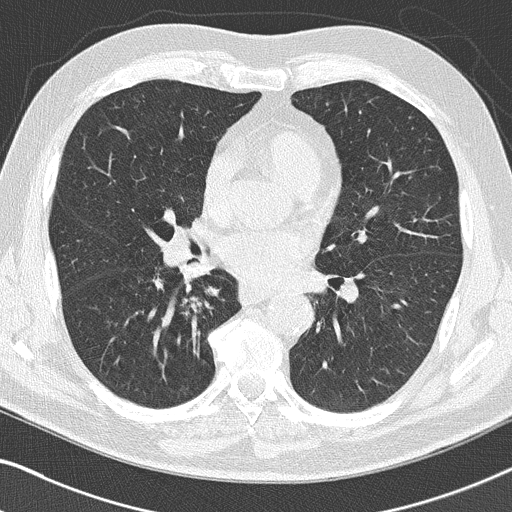
Axial slice from a low-dose chest CT screening exam; third screening round (two years after baseline); lung window (W 1500 / L -600 HU); slice 89 of 155 in the series. Male participant, aged 66 years at enrolment.
Expert-annotated lung lesion, box from (x=138, y=265) to (x=229, y=328) px. The exam's reader record, not a measurement of the box and not confirmed to be the same lesion: non-calcified nodule or mass ≥4 mm, right upper lobe, 5 × 4 mm, smooth margins, pre-existing on the prior screen: yes; interval growth: no. Participant outcome: lung cancer diagnosed 38 days after this screen — squamous cell carcinoma, NOS, right lower lobe, poorly differentiated (G3), stage IIA (AJCC 6th edition), 22 mm at pathology.